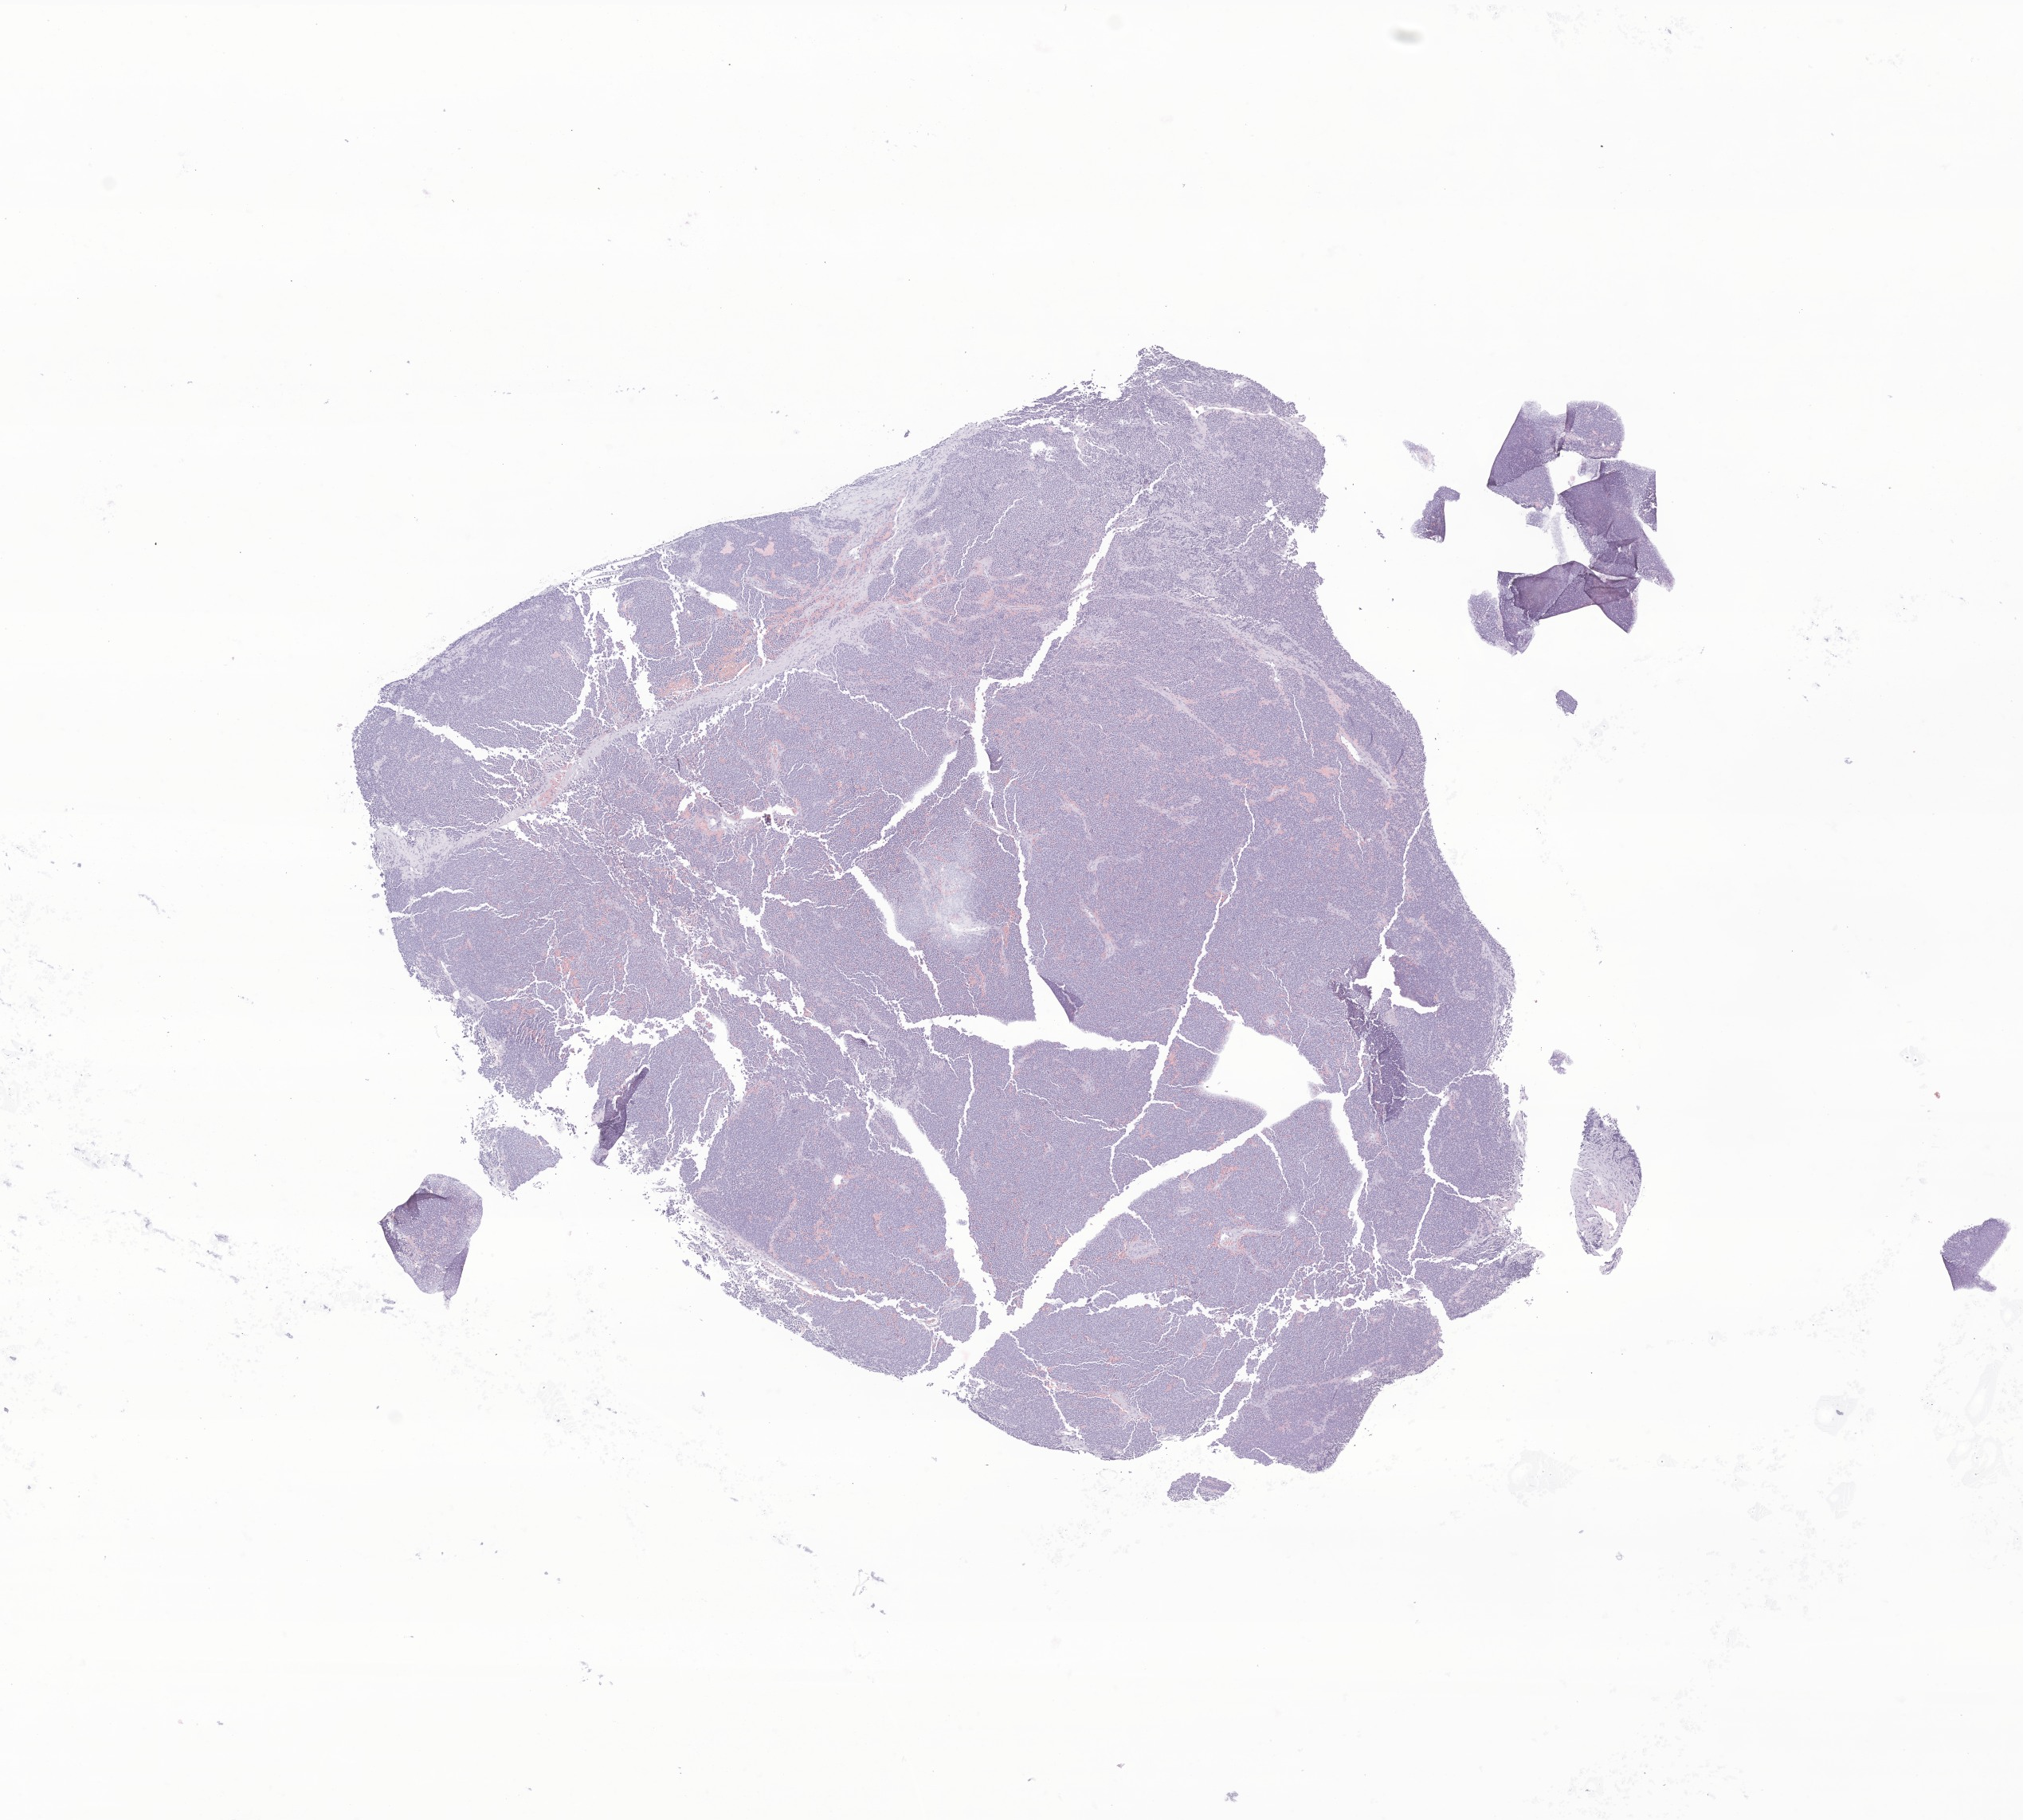
Whole-slide image, H&E stain of tumor tissue from the abdomen — a low-resolution overview of the entire scanned area, about 10.7 x 9.6 mm; formalin-fixed, paraffin-embedded (FFPE) tissue. Patient: male, age 43 months (3 years 7 months).
Recorded diagnosis: Neuroblastoma, NOS.